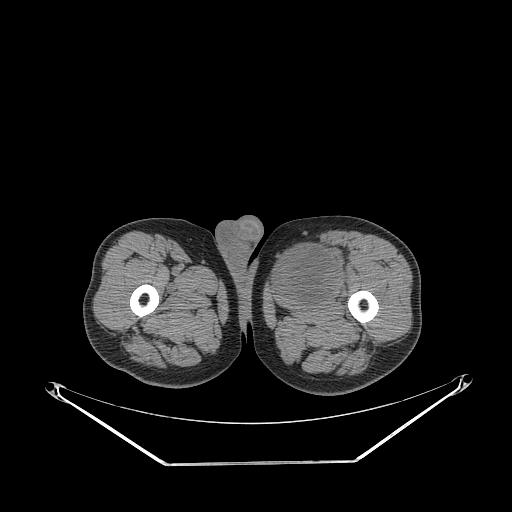
CT of an extremity soft-tissue mass (from a PET/CT study), one axial slice. Soft-tissue window (W 400 / L 40 HU). 3.75 mm slice thickness. 512 × 512 image matrix, field of view 500 × 500 mm. Male patient. Case-level facts recorded for this patient, not image findings: histological type: pleiomorphic liposarcoma; grade: high; site of the primary tumour: left thigh.
Structures marked on this image (expert contour drawn on MRI and transferred to this co-registered scan by the dataset authors):
- gross tumour volume including surrounding oedema: box from (x=279, y=240) to (x=346, y=296) px
- gross tumour volume (mass): (x=279, y=247)–(x=337, y=296)